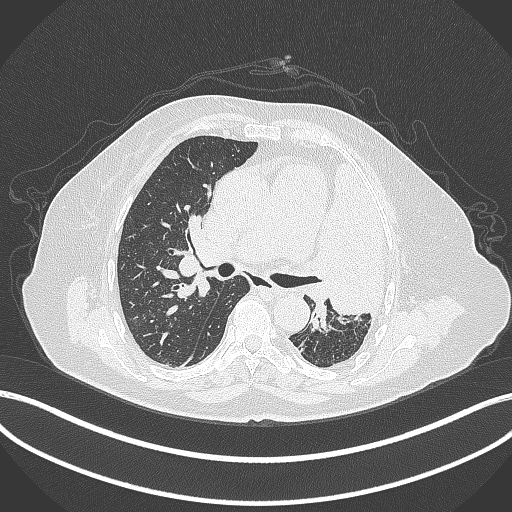
Chest CT, one axial slice; position 233 of 399 along the scan axis; lung window (W 1500 / L -600 HU); 1 mm slice thickness; 512 × 512 image matrix, field of view 400 × 400 mm. Patient: female, 75 years. From the clinical record (not read from this slice): clinical TNM (as recorded): T3 N3 M1.
Structures marked on this image (rectangle marked by the reading radiologist):
- lung tumour (recorded histology: adenocarcinoma): box from (x=317, y=159) to (x=392, y=322) px